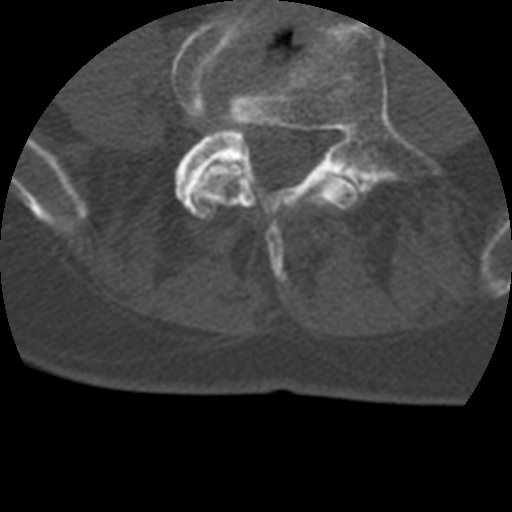
CT including the spine, one axial slice; slice 52 of 399 in the series (ordered by position); reconstruction kernel STANDARD; bone window (W 1800 / L 400 HU); 512 × 512 image matrix, field of view 160 × 160 mm. Patient age 69 years. From the clinical record (not read from this slice): primary cancer: prostate.
Outlined on this slice (semi-automatic segmentation, software-assisted and operator-edited):
- L4 vertebra: bounding box <171,11,361,282> (left, top, right, bottom; pixels)
- L5 vertebra: <175,22,432,211>